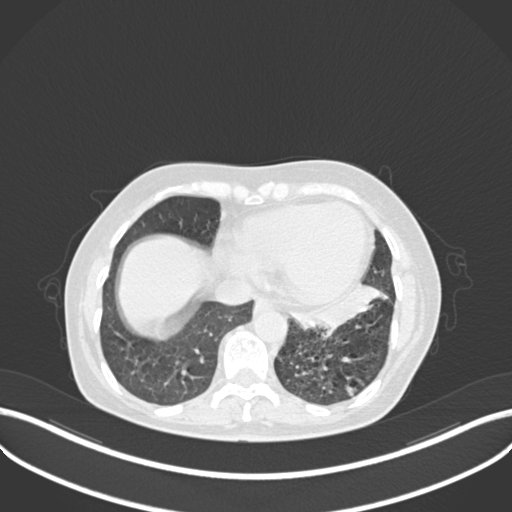
Chest CT, one axial slice. Position 74 of 270 along the scan axis. 120 kVp. Lung window (W 1500 / L -600 HU). 1 mm slice thickness. 512 × 512 image matrix, field of view 400 × 400 mm. Patient: female, 63 years. Case-level facts recorded for this patient, not image findings: clinical TNM (as recorded): T1b N0 M0.
Outlined on this slice (rectangle marked by the reading radiologist):
- lung tumour (recorded histology: adenocarcinoma): bounding box <282,283,388,335> (left, top, right, bottom; pixels)